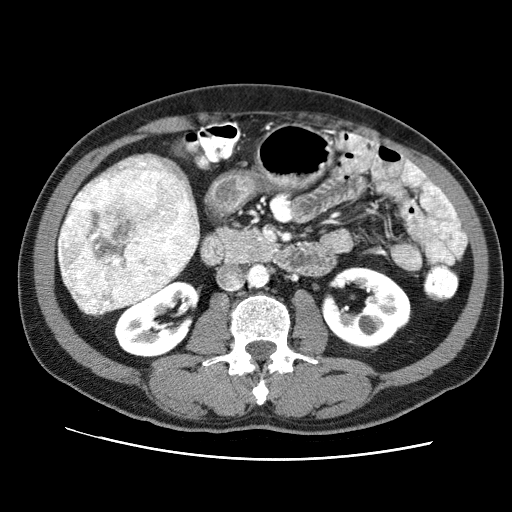
Contrast-enhanced abdominal CT (liver protocol), one axial slice; position 23 of 71 along the scan axis; reconstruction kernel STANDARD; soft-tissue window (W 400 / L 40 HU); 2.5 mm slice thickness; 512 × 512 image matrix. From the clinical record (not read from this slice): diagnosis: hepatocellular carcinoma (patient treated with transarterial chemoembolisation; whether this scan precedes or follows treatment is not stated here); TNM stage (as recorded): Stage-II; Child-Pugh class: A; tumour differentiation: well differentiated; tumour nodularity: multinodular.
Outlined on this slice (semi-automatically segmented with operator editing):
- liver parenchyma outside the tumour (the mass and vessels are separate outlines, so this box may not span the whole liver): box from (x=58, y=152) to (x=200, y=311) px
- mass: (x=57, y=165)–(x=200, y=315)
- liver vessels: (x=114, y=157)–(x=162, y=174)